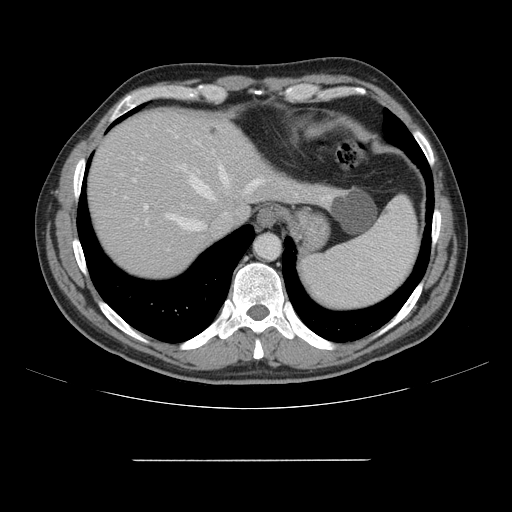
Contrast-enhanced abdominal CT, one axial slice; slice 129 of 164 in the series (ordered by position); intravenous contrast given; soft-tissue window (W 400 / L 40 HU); 2.5 mm slice thickness; 512 × 512 image matrix, field of view 404 × 404 mm. Male patient, age 54 years. Case-level facts recorded for this patient, not image findings: diagnosis: colorectal cancer liver metastases, imaged before liver resection.
Annotated regions visible in this slice (expert manual segmentation):
- hepatic veins: box from (x=166, y=166) to (x=262, y=231) px
- liver: (x=89, y=110)–(x=330, y=277)
- planned liver remnant (the part of the liver to remain after resection): (x=89, y=110)–(x=254, y=277)
- portal vein (with intrahepatic branches): (x=133, y=157)–(x=148, y=223)